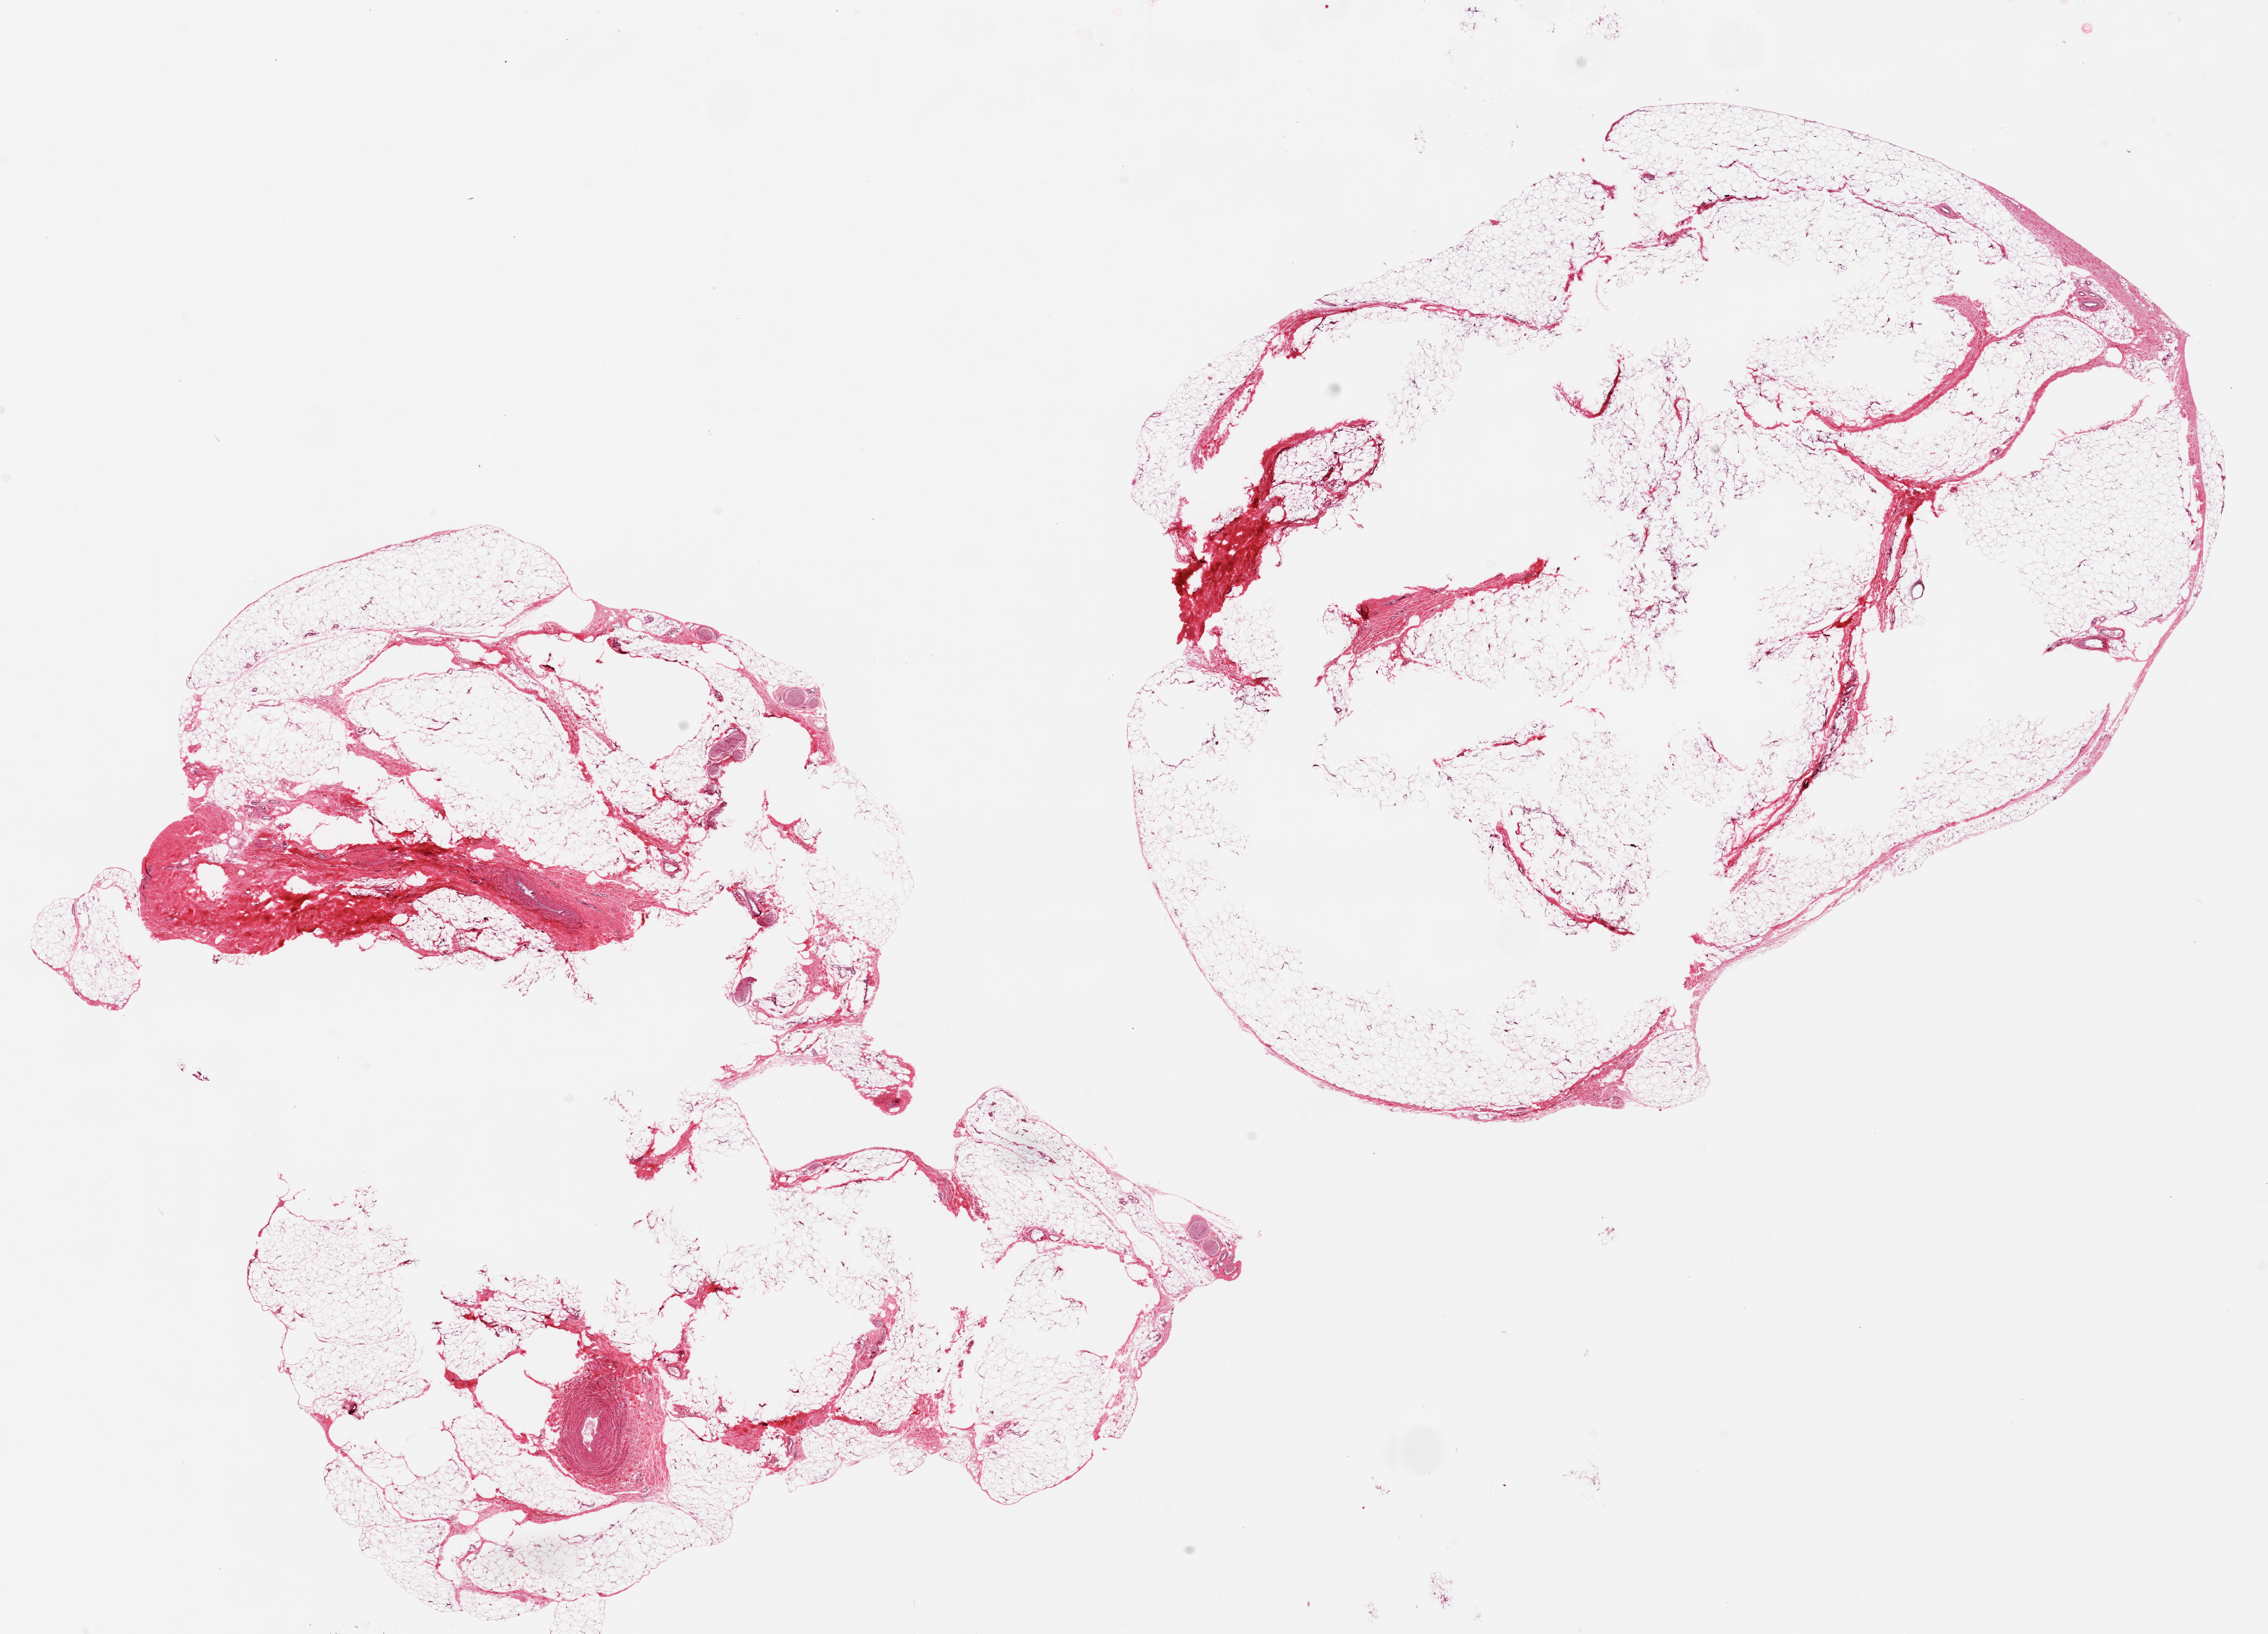
Digitized H&E-stained section — shown as a low-resolution overview of the whole scanned area (about 25.6 x 18.4 mm, from a 20x scan), PAXgene-fixed paraffin-embedded (PFPE) section, sampled site (target tissue): adipose tissue, tissue donor sample.
Reviewer comment on this tissue sample: 2 pieces, 13x9 & 13x8 mm; large central defects, probably poorly fixed in these large aliquots.